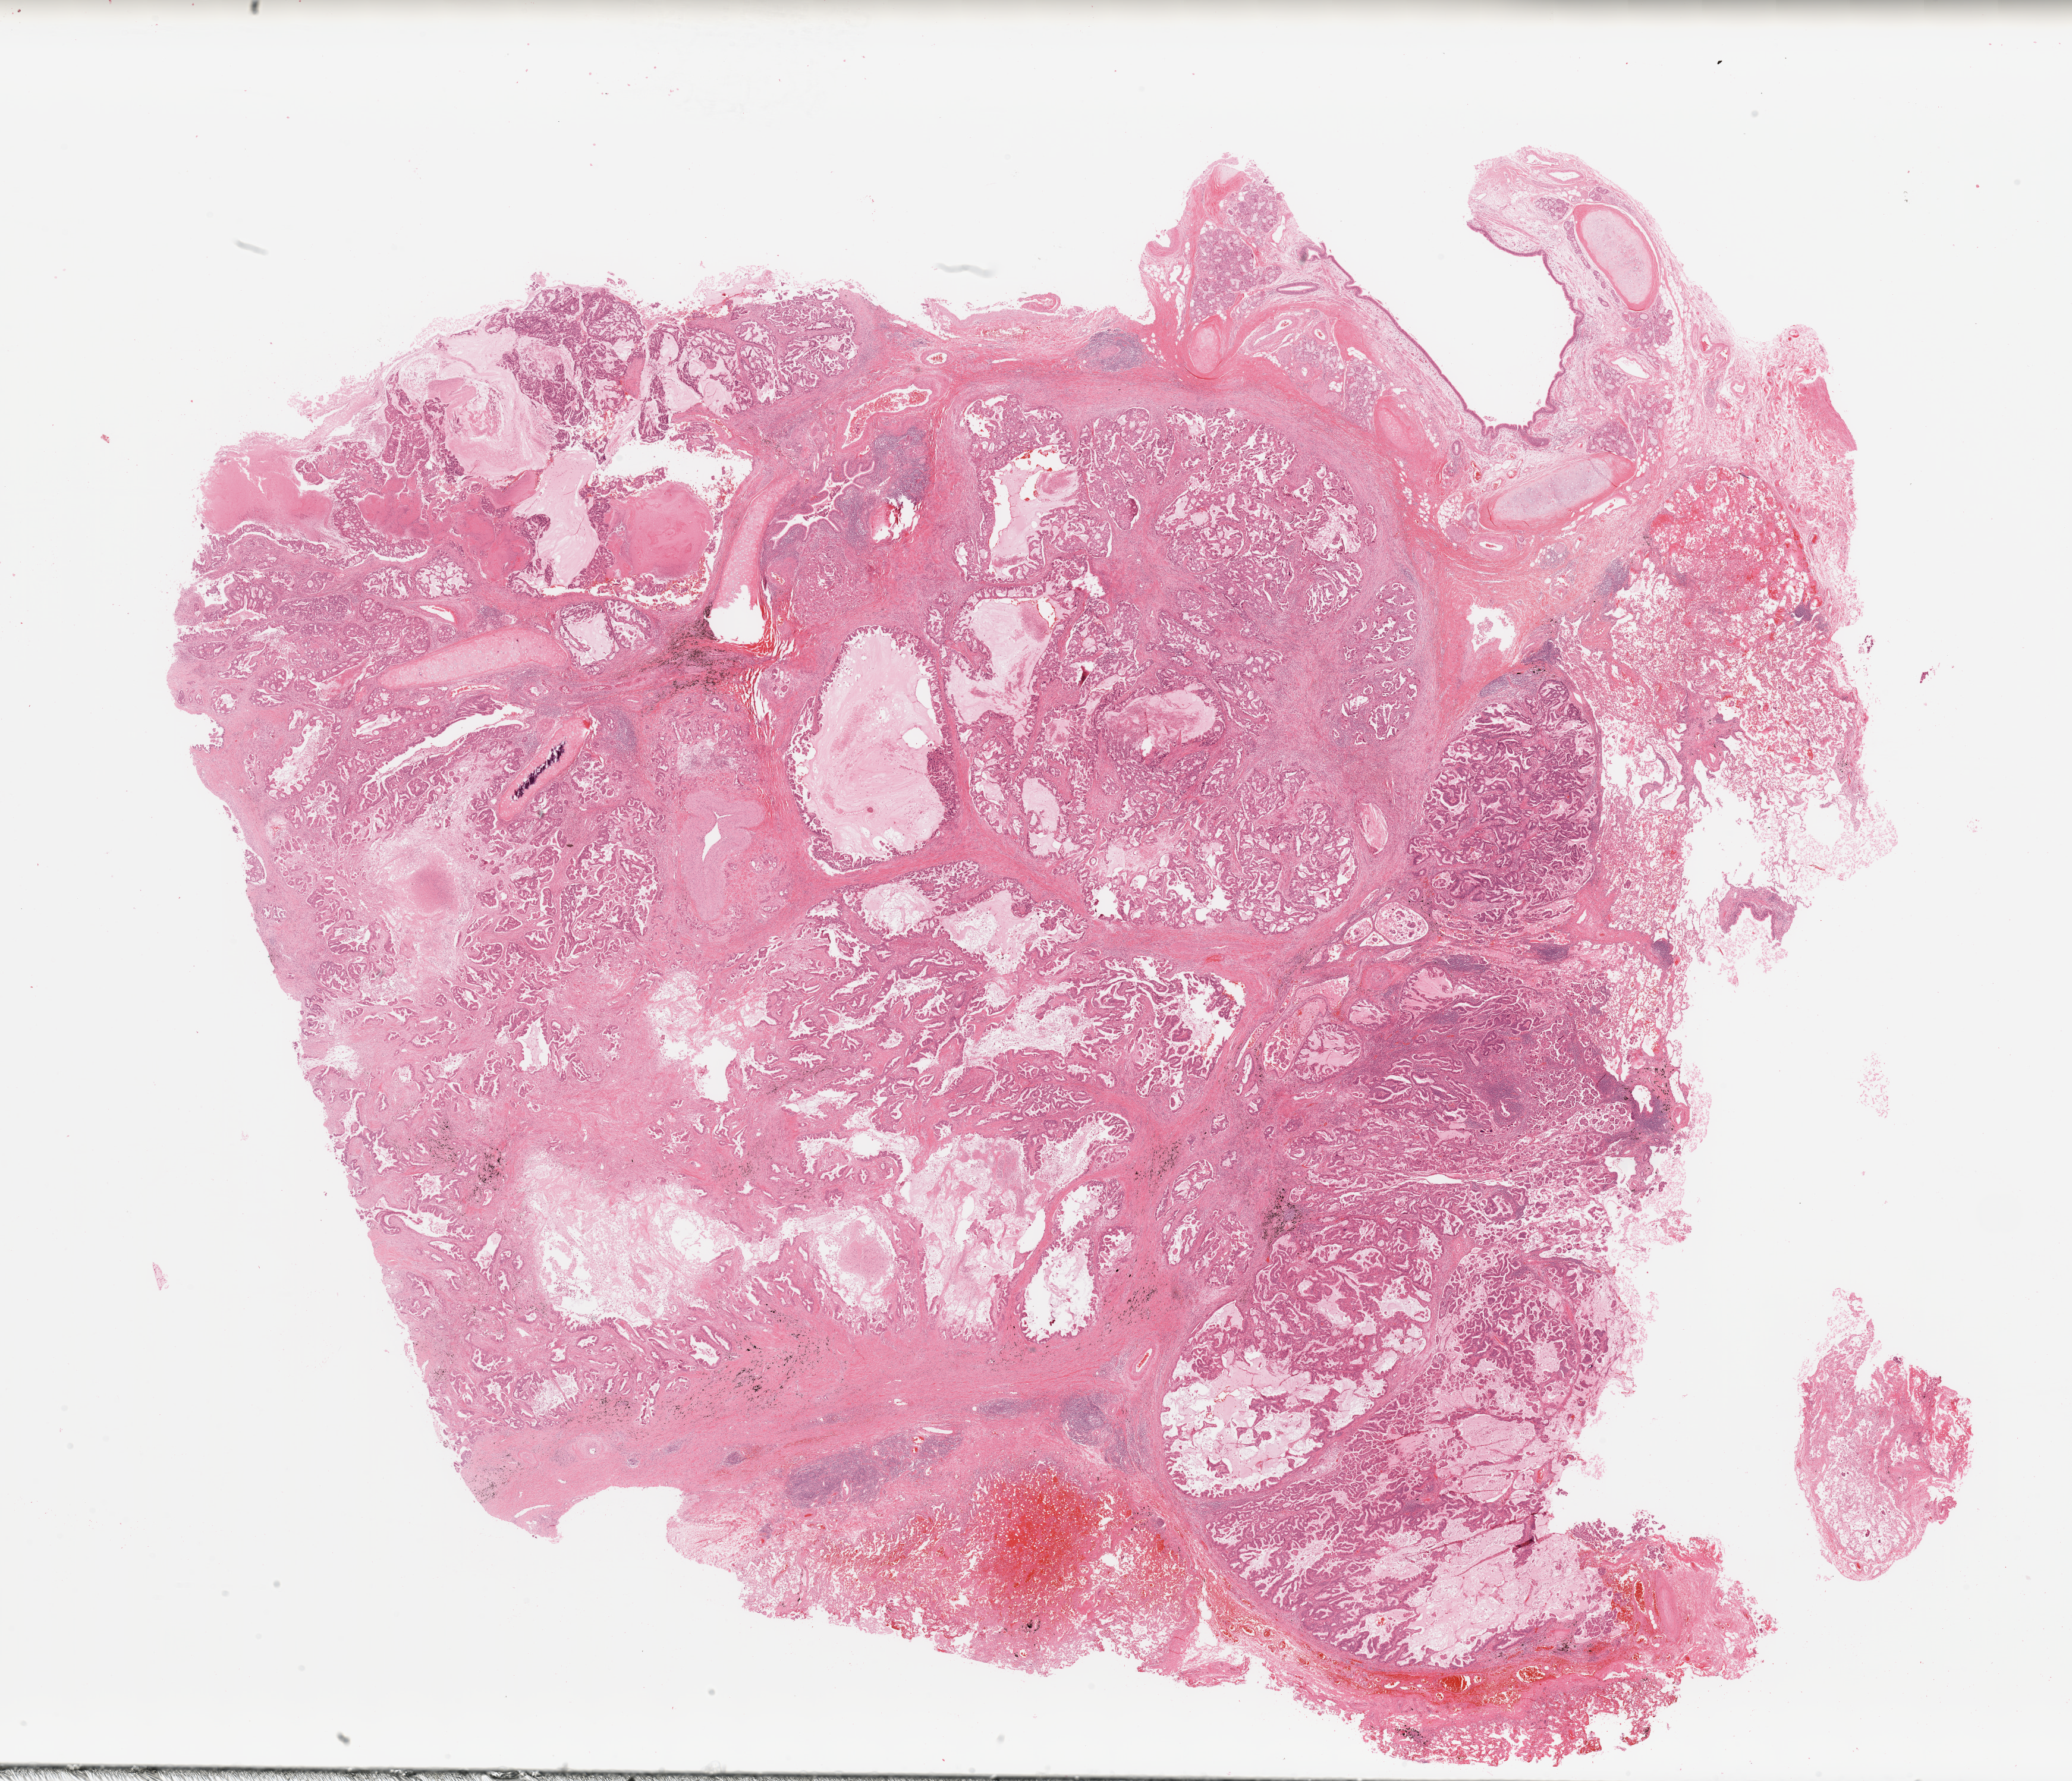
Whole-slide histology image, Hematoxylin and eosin (H&E) stained, low-resolution overview of the scanned area, about 27.6 x 23.7 mm; lung, tumour tissue. Male, 63 y/o. Histologic grade: G2 (moderately differentiated).
Histologic diagnosis: Adenocarcinoma, NOS.